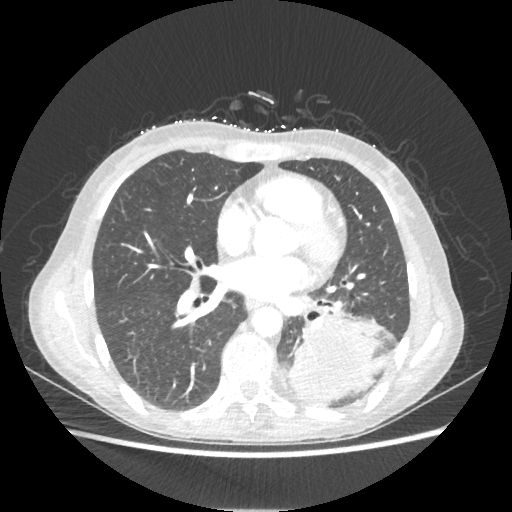
Chest CT, one axial slice. Slice 103 of 221 in the series (ordered by position). 80 kVp. Lung window (W 1500 / L -600 HU). 1.25 mm slice thickness. 512 × 512 image matrix, field of view 360 × 360 mm. Female patient, age 53 years. Case-level facts recorded for this patient, not image findings: clinical TNM (as recorded): T3 N0 M0.
Annotated regions visible in this slice (bounding box drawn by a radiologist):
- lung tumour (recorded histology: adenocarcinoma): bounding box [x1, y1, x2, y2] px = [287, 315, 387, 407]